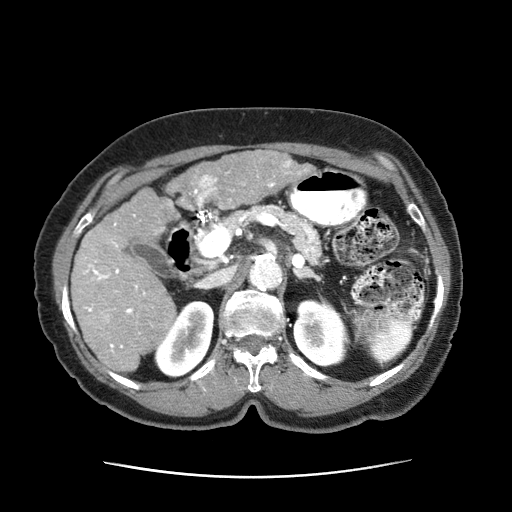
Contrast-enhanced abdominal CT (liver protocol), one axial slice. Position 26 of 63 along the scan axis. 120 kVp. Intravenous contrast given. Soft-tissue window (W 400 / L 40 HU). 2.5 mm slice thickness. 512 × 512 image matrix, field of view 360 × 360 mm. Female patient, age 79 years. From the clinical record (not read from this slice): diagnosis: hepatocellular carcinoma (patient treated with transarterial chemoembolisation; whether this scan precedes or follows treatment is not stated here); TNM stage (as recorded): Stage-II; Child-Pugh class: B; tumour differentiation: well differentiated; tumour nodularity: multinodular.
Outlined on this slice (semi-automatic segmentation, software-assisted and operator-edited):
- abdominal aorta: bounding box [x1, y1, x2, y2] px = [249, 253, 281, 290]
- liver parenchyma outside the tumour (the mass and vessels are separate outlines, so this box may not span the whole liver): [71, 189, 181, 375]
- mass: [167, 152, 313, 208]
- necrosis: [205, 181, 207, 183]
- liver vessels: [83, 172, 289, 353]